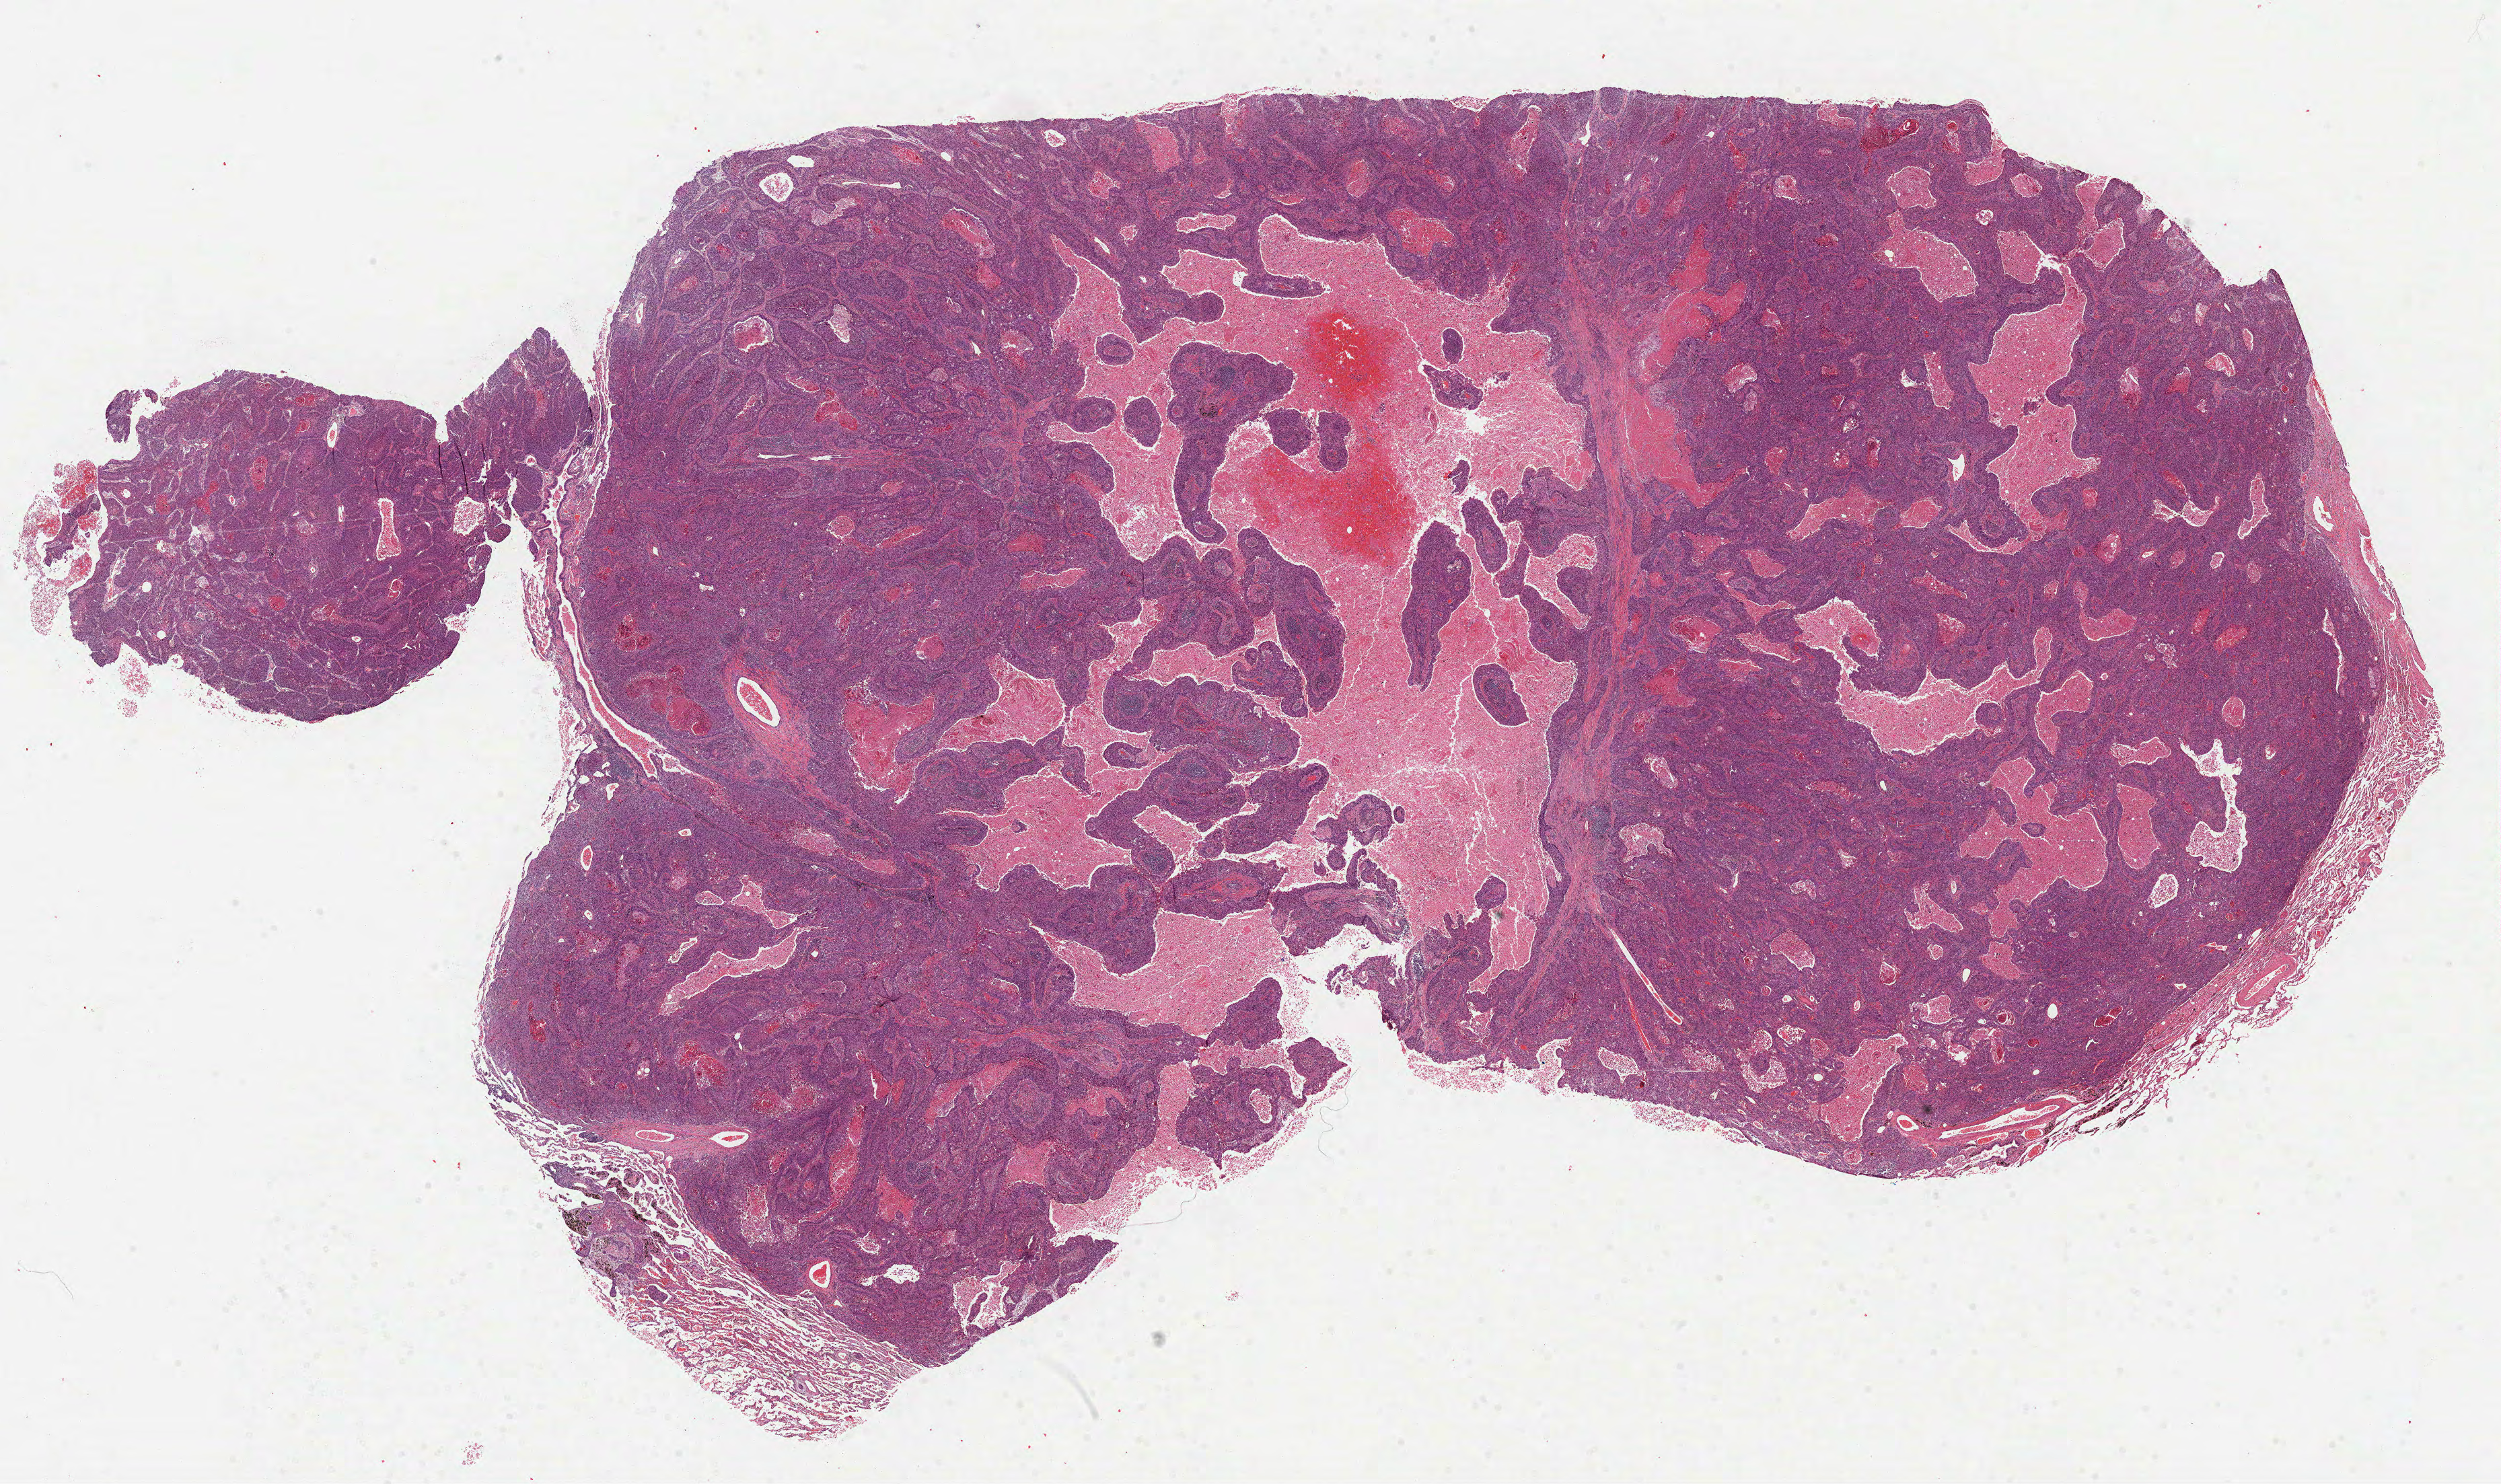
H&E whole-slide image, shown as a low-resolution overview of the whole scanned area (about 30.0 x 17.8 mm, slide scanned at 40x). Formalin-fixed paraffin-embedded (FFPE) diagnostic section. Sample: primary tumour, lung. Male patient; age at initial diagnosis 65 years.
AJCC pathologic stage: IIIB. Laterality: right. Pathologic diagnosis: Basaloid squamous cell carcinoma.